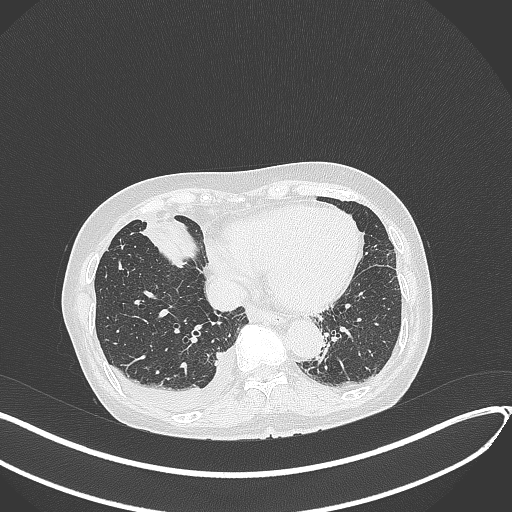
Chest CT, one axial slice; slice 112 of 418 in the series (ordered by position); reconstruction kernel B70f; 120 kVp; lung window (W 1500 / L -600 HU); 1 mm slice thickness; 512 × 512 image matrix. Patient: female, 75 years. From the clinical record (not read from this slice): clinical TNM (as recorded): T2a N3 M0.
Annotated regions visible in this slice (bounding box drawn by a radiologist):
- lung tumour (recorded histology: adenocarcinoma): bounding box (x1, y1, x2, y2) in pixels: (138, 216, 202, 271)